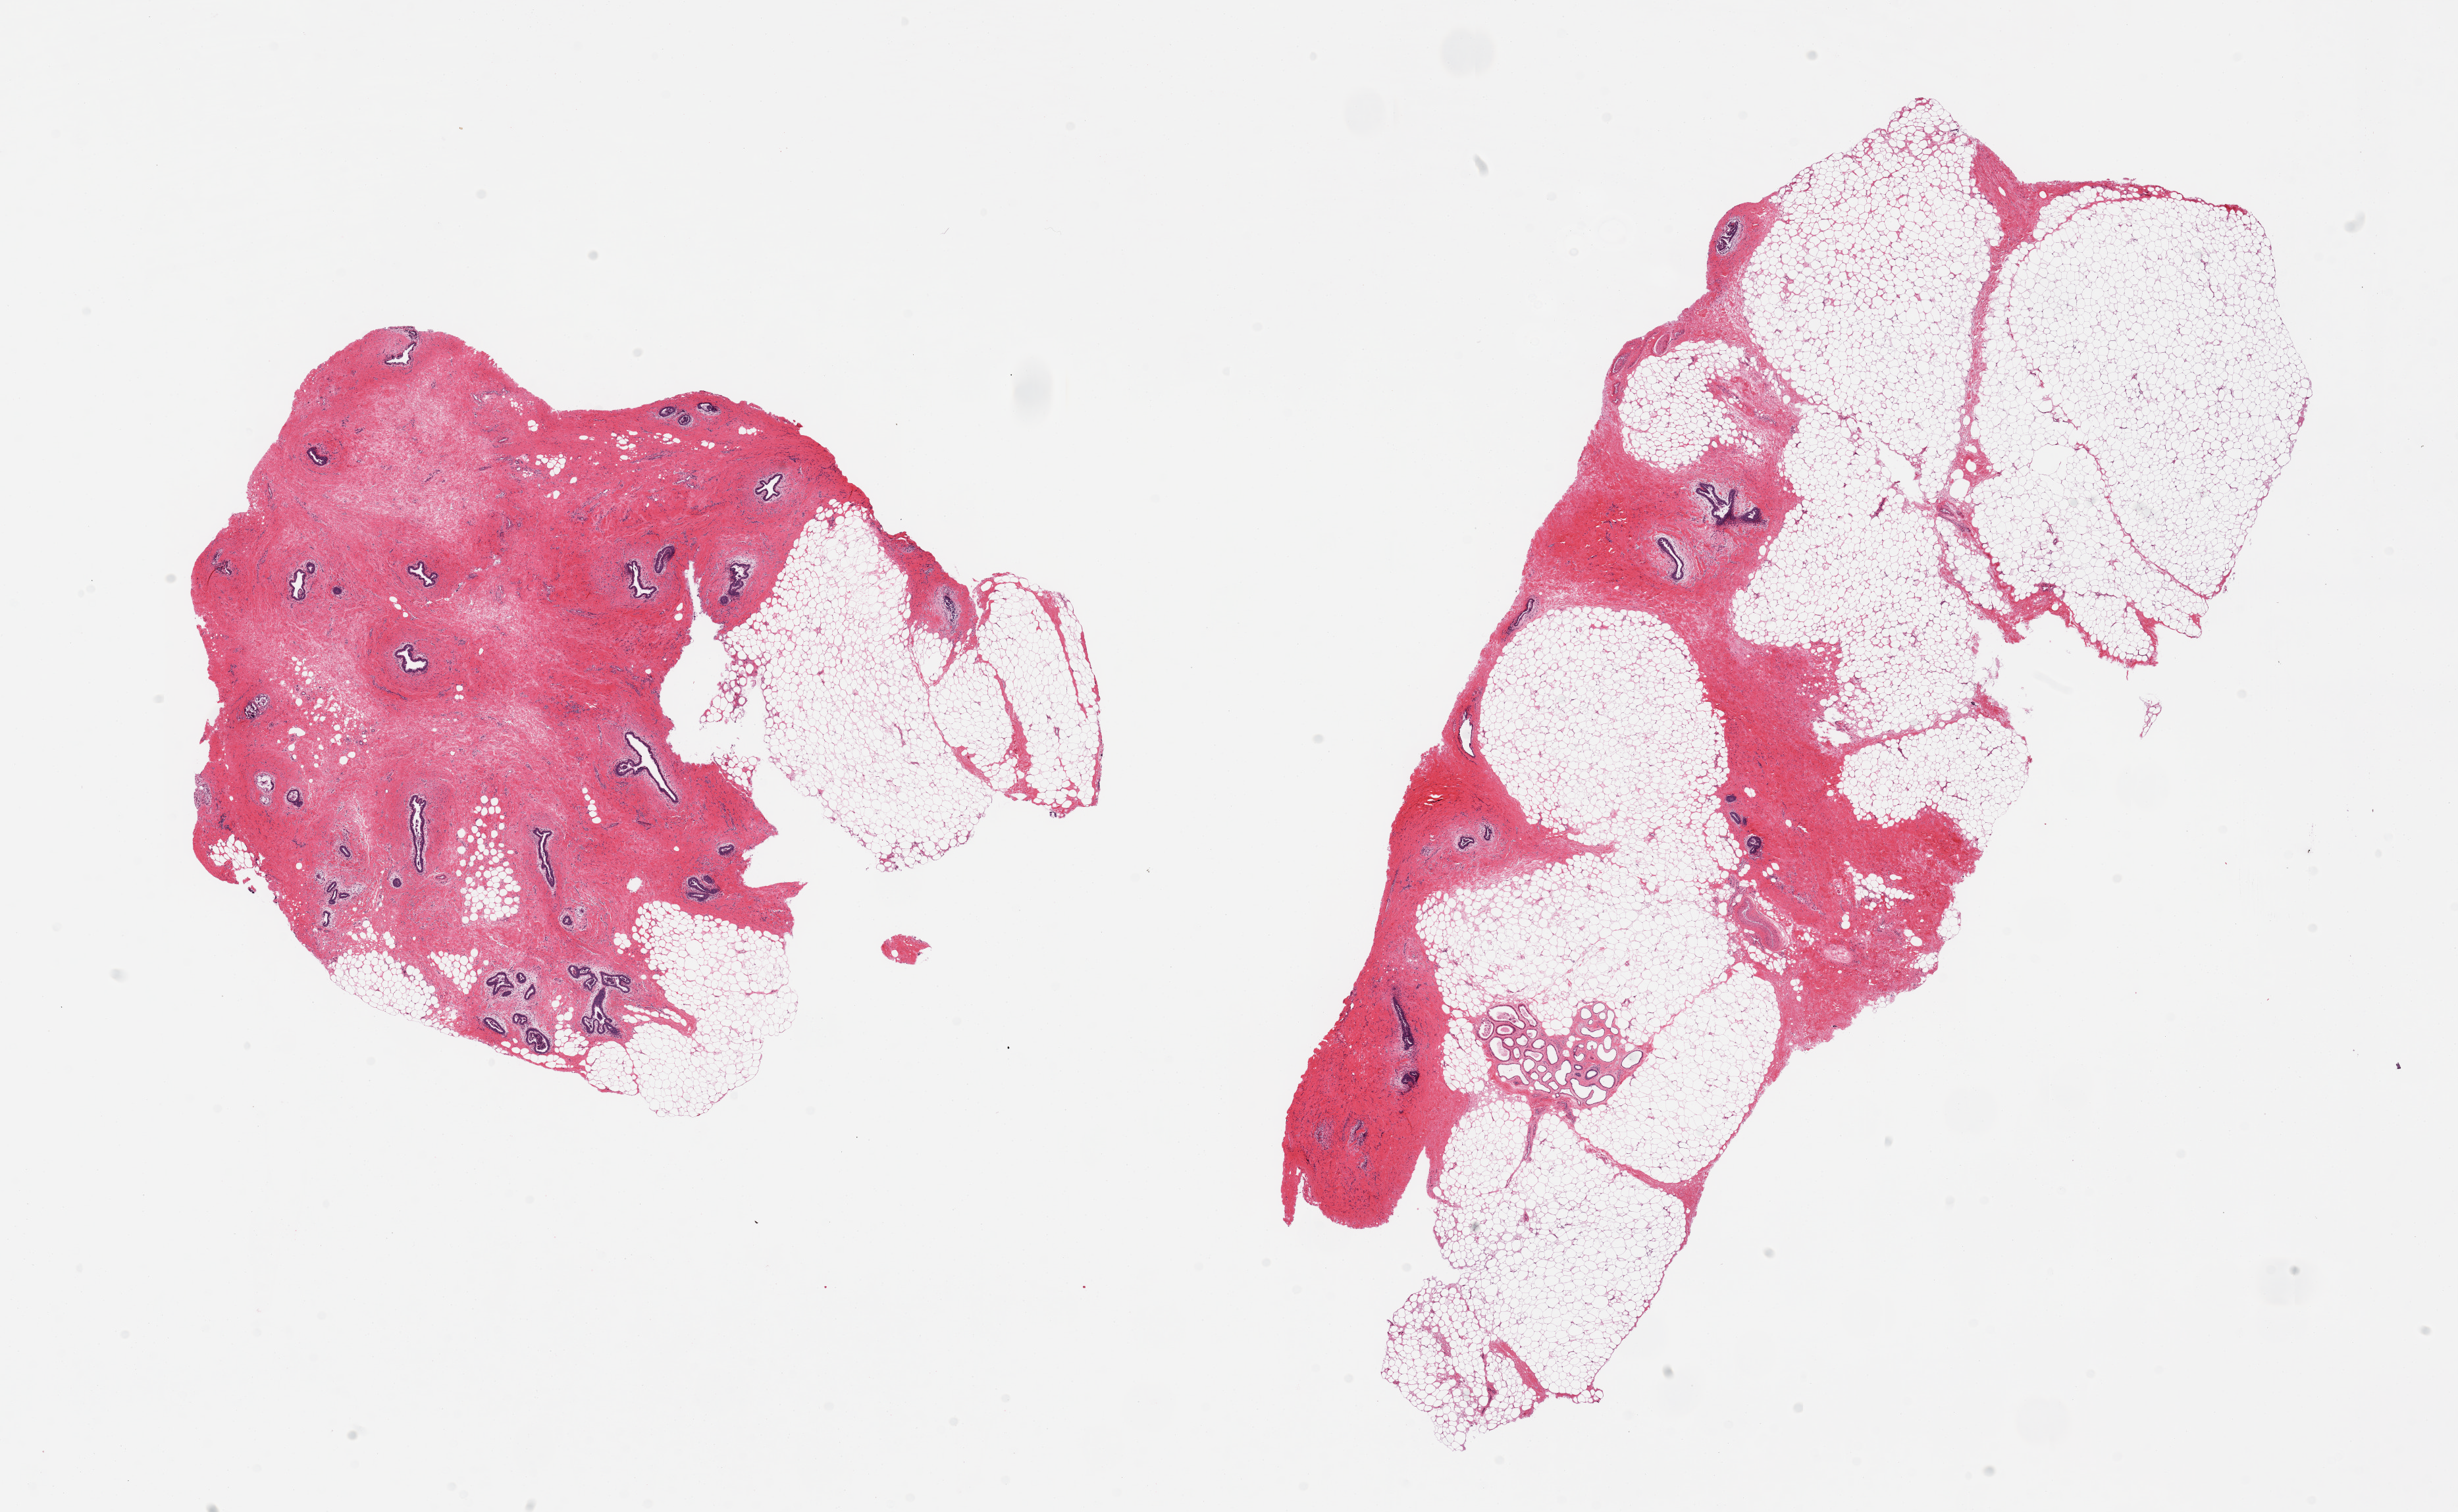
Digitized H&E-stained section, brightfield, low-resolution overview of the scanned area, about 29.5 x 18.2 mm (from a 20x scan); PAXgene-fixed, paraffin-embedded tissue; sampled site (target tissue): breast; tissue donor sample. Male donor.
* pathologist's review note for this sample: 2 pieces prominent stromal and ductal gynecomastoid hyperplasia